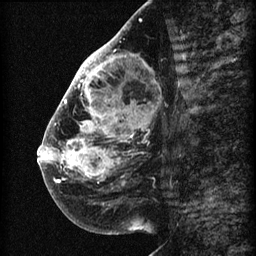
Breast MRI (dynamic contrast-enhanced), one sagittal slice. Position 28 of 60 along the scan axis. 3 images stored at this slice position (order not interpretable as contrast timing). 1.5 T. TE 4.2 ms, TR 22.7 ms. 2 mm slice thickness. 256 × 256 image matrix. Patient: female, 48 years. Case-level facts recorded for this patient, not image findings: setting: breast cancer imaged before/during neoadjuvant chemotherapy; receptor status: triple-negative.
Outlined on this slice (semi-automatically segmented with operator editing):
- analysis volume of interest (the breast-tissue region the enhancement analysis was run in; not a lesion): box from (x=44, y=30) to (x=173, y=207) px
- tumour enhancement mask (voxels above the 90 % enhancement threshold inside the analysis volume of interest): (x=44, y=30)–(x=125, y=189)